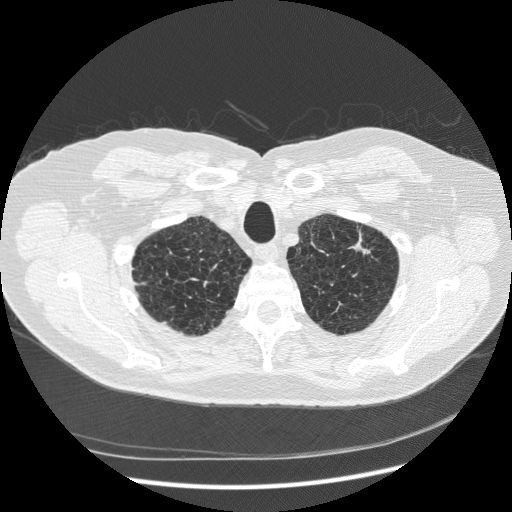
Chest CT (low-dose screening protocol), one axial image. Baseline screening round. Lung window (W 1500 / L -600 HU). 1.25 mm slice thickness. Standard (soft-tissue) reconstruction kernel (STANDARD). 120 kVp. Slice 36 of 265 in the series. Male participant, aged 70 years at enrolment. Former smoker at enrolment.
Expert-annotated lung lesion, bounding box [x1, y1, x2, y2] px = [333, 220, 389, 276]. The screening reader recorded 2 non-calcified nodules or masses ≥4 mm on this exam (right lower lobe, right lower lobe); which of them this box marks is not recorded. Official screen result: positive, change unspecified: nodule(s) >= 4 mm or enlarging nodule(s), mass(es), or other non-specific abnormalities suspicious for lung cancer. Participant outcome: lung cancer diagnosed 816 days after this screen — squamous cell carcinoma, NOS, left upper lobe, moderately differentiated (G2), stage IA (AJCC 6th edition), 18 mm at pathology.